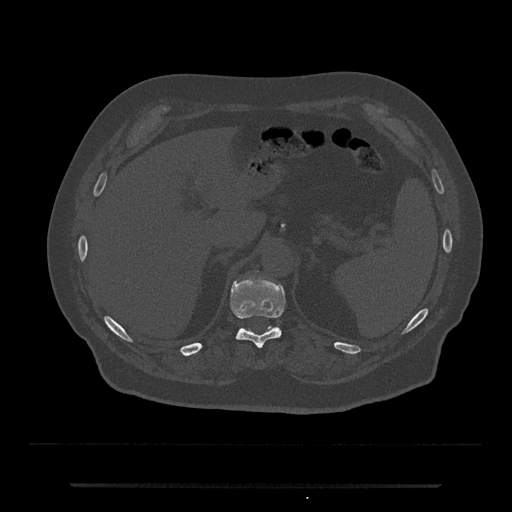
CT including the spine, one axial slice; position 644 of 797 along the scan axis; reconstruction kernel Br40s/3; bone window (W 1800 / L 400 HU); 0.5 mm slice thickness; 512 × 512 image matrix, field of view 434 × 434 mm. Male patient, age 80 years. From the clinical record (not read from this slice): primary cancer: prostate.
Structures marked on this image (semi-automatic segmentation, software-assisted and operator-edited):
- T11 vertebra: bounding box (x1, y1, x2, y2) in pixels: (230, 280, 285, 349)